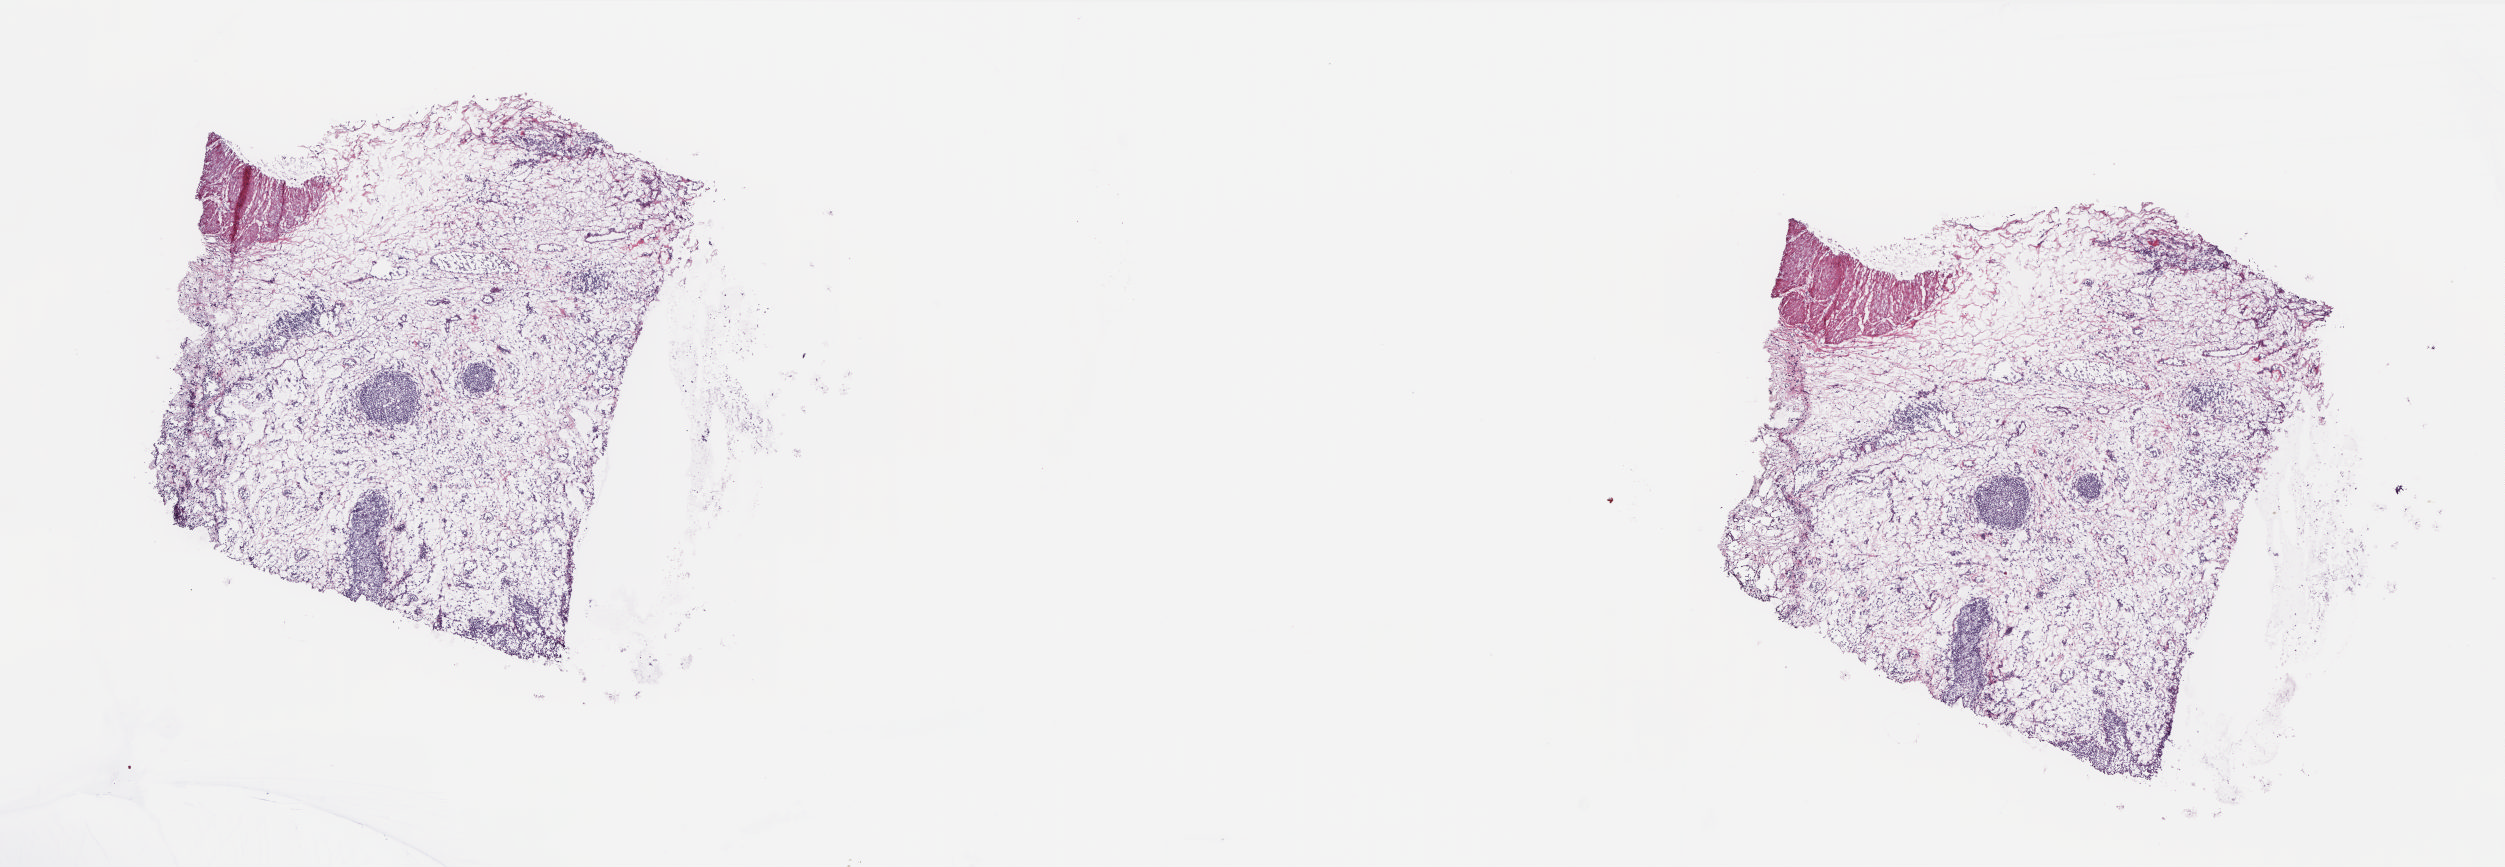
Whole-slide histology image, Hematoxylin and eosin (H&E) stained, whole scanned area (about 20.2 x 7.0 mm) shown as a low-resolution overview, frozen section, bladder, solid tissue normal (non-tumour tissue) sample. Male, age 69 years at initial diagnosis. Pathologist review of this section (percent, as recorded): tumour cells 0%, tumour nuclei 0%.
This section: solid tissue normal sample (biorepository sample class). Patient diagnosis: Transitional cell carcinoma (trigone of bladder).